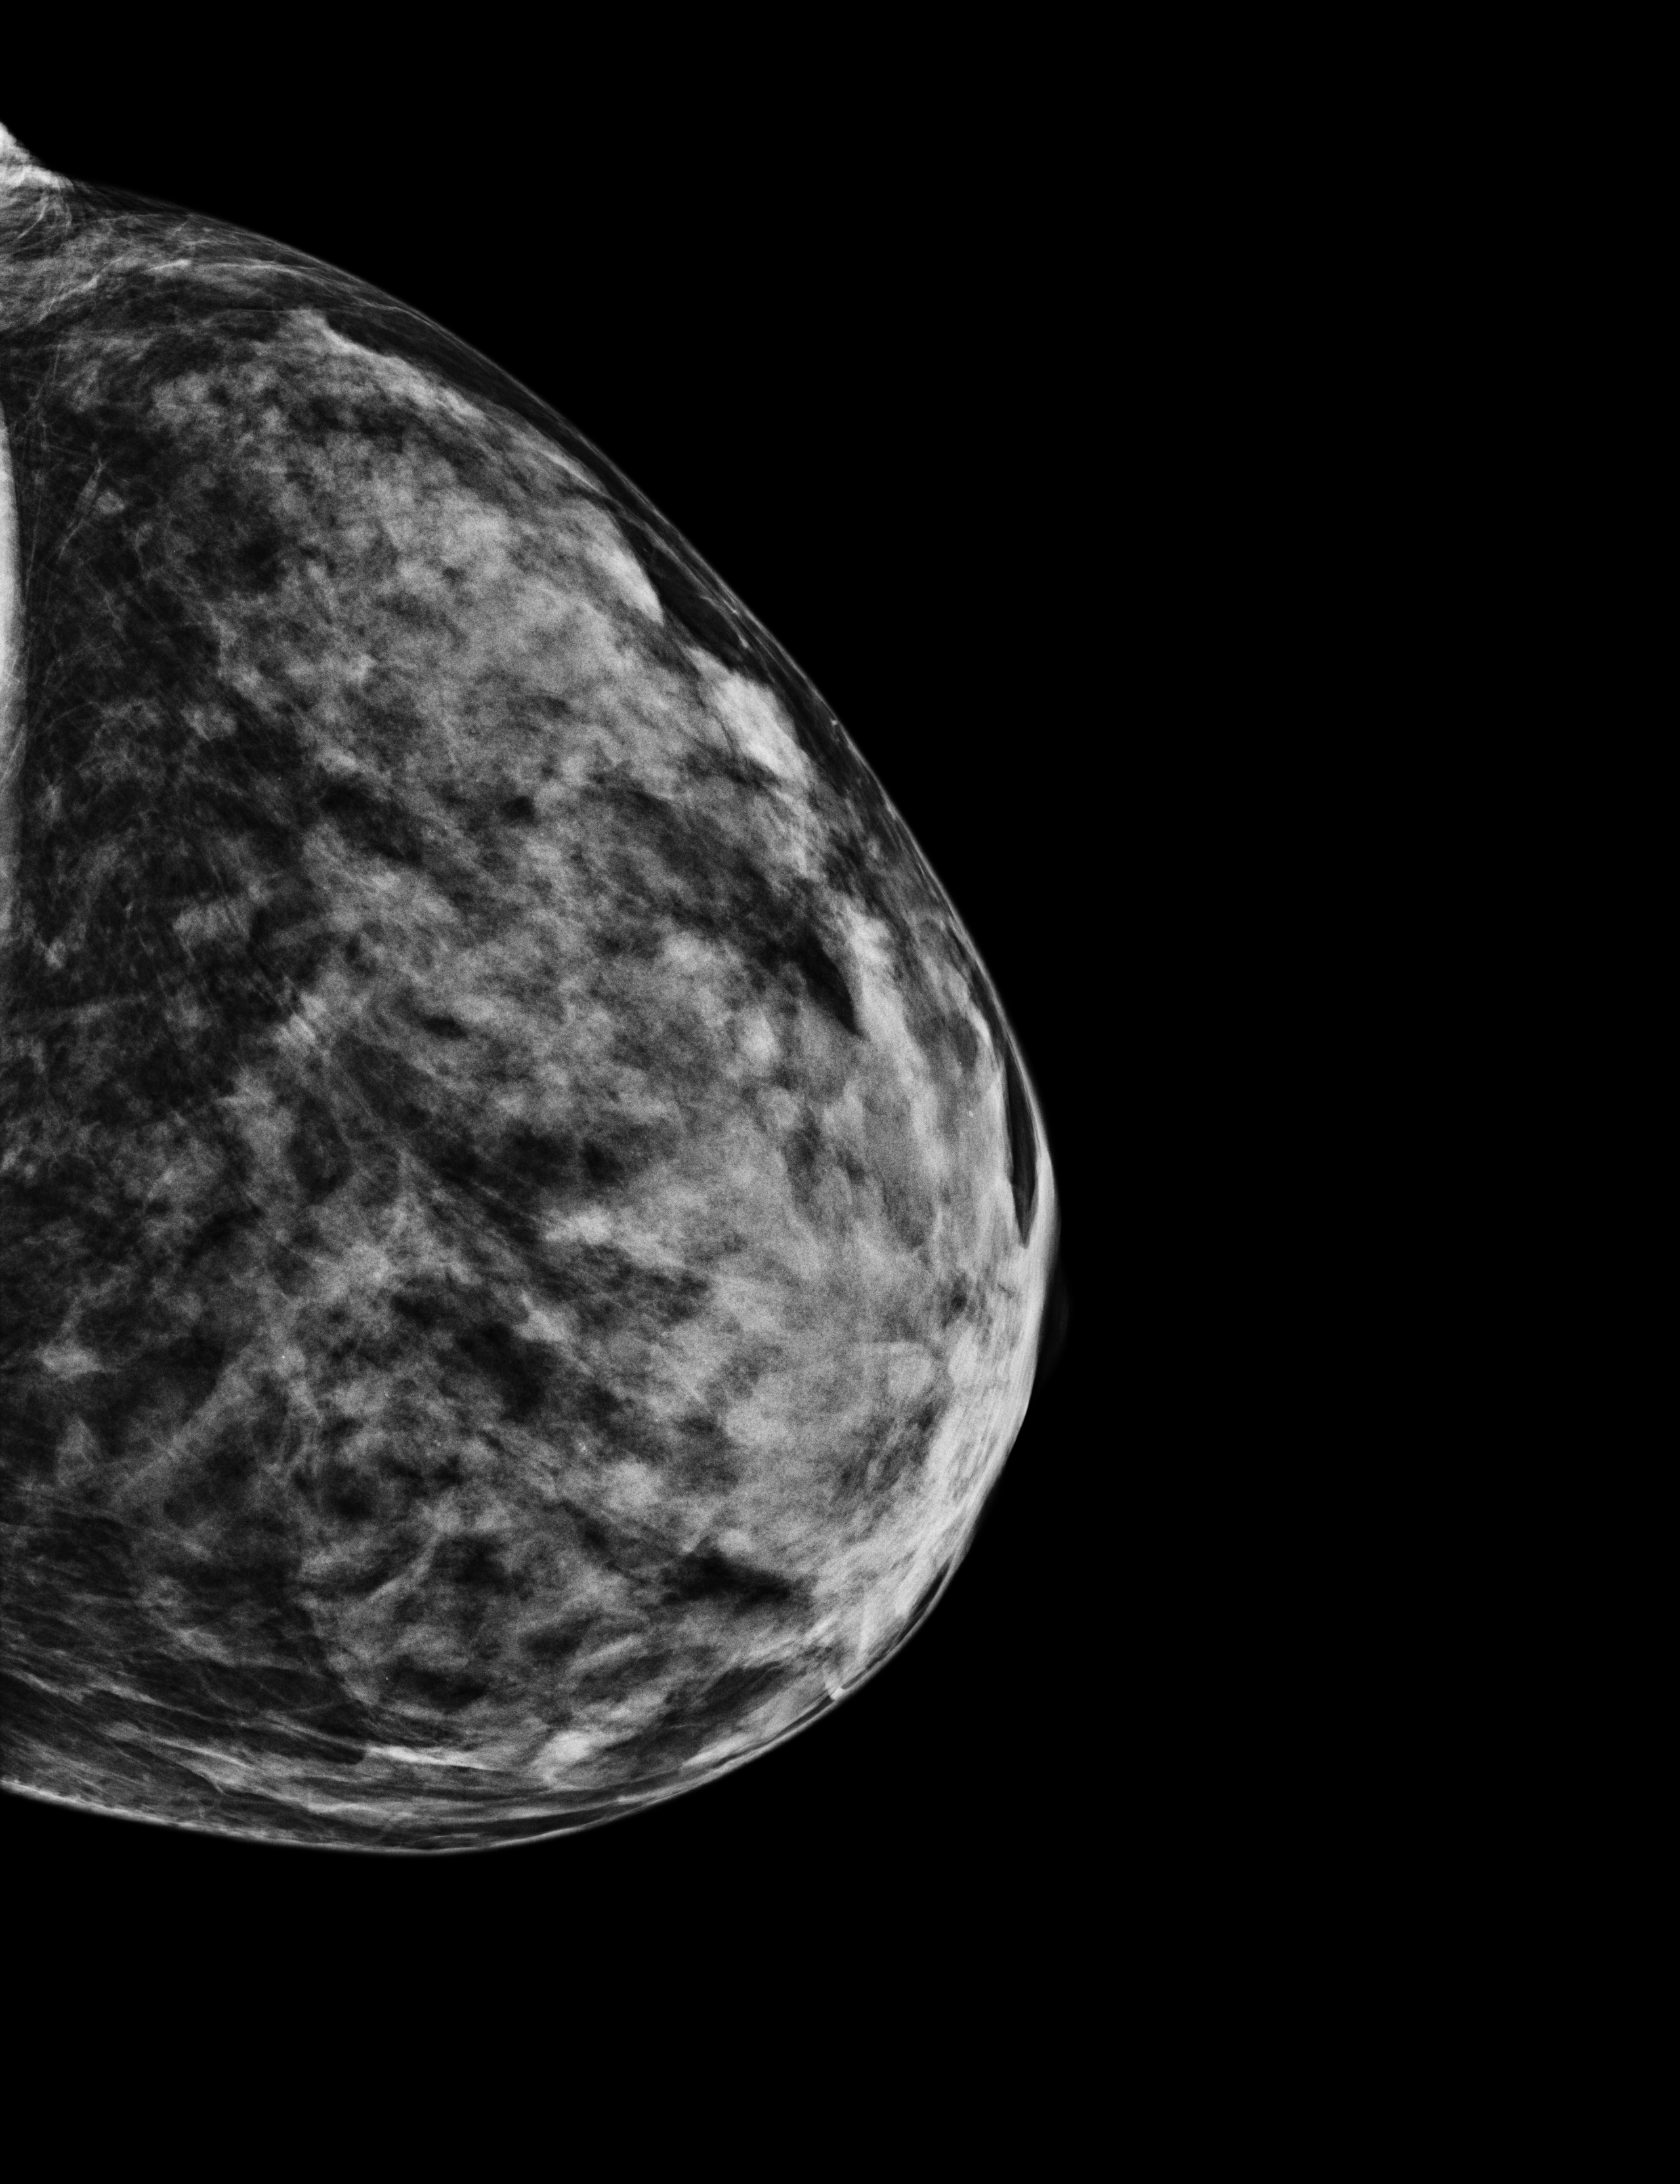
Digital mammogram (FFDM), left breast, exaggerated CC view (lateral), screening examination. Patient: female, 43 years.
Breast density at the screening exam (both breasts): extremely dense (BI-RADS density category d). Final BI-RADS assessment for this screening round (tomosynthesis exam, both breasts): category 2. Recall: no recall after this screen.